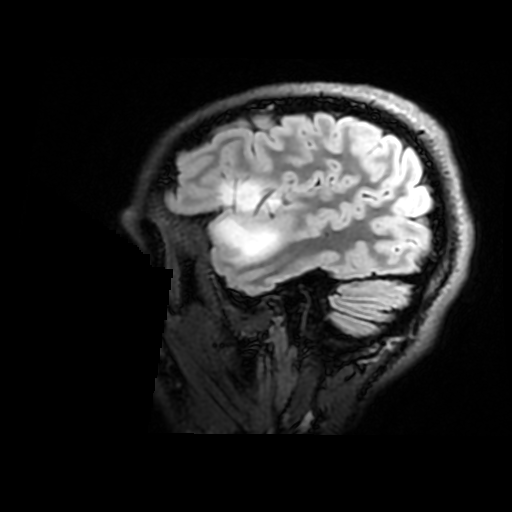
Brain MRI from a brain-tumour surgery series, one sagittal slice; slice 137 of 176 in the series (ordered by position); T2 FLAIR; 1 mm slice thickness; 512 × 512 image matrix. Case-level facts recorded for this patient, not image findings: histopathology: Astrocytoma; WHO grade: 2; IDH mutation: yes.
Structures marked on this image (outlined manually by an expert reader):
- tumour: bounding box (x1, y1, x2, y2) in pixels: (220, 181, 282, 262)